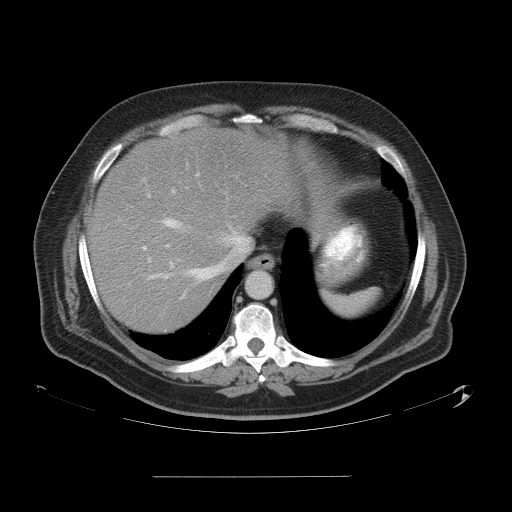
Contrast-enhanced abdominal CT, one axial slice. Position 46 of 58 along the scan axis. Soft-tissue window (W 400 / L 40 HU). 5 mm slice thickness. 512 × 512 image matrix, field of view 480 × 480 mm. Male patient, age 63 years. Case-level facts recorded for this patient, not image findings: diagnosis: colorectal cancer liver metastases, imaged before liver resection; multiple liver metastases: no; largest metastasis: 4.2 cm; disease in both lobes: no.
Annotated regions visible in this slice (manually delineated by an expert):
- hepatic veins: bounding box (x1, y1, x2, y2) in pixels: (147, 194, 247, 300)
- liver: (90, 129, 295, 332)
- planned liver remnant (the part of the liver to remain after resection): (90, 201, 226, 332)
- portal vein (with intrahepatic branches): (143, 173, 200, 250)